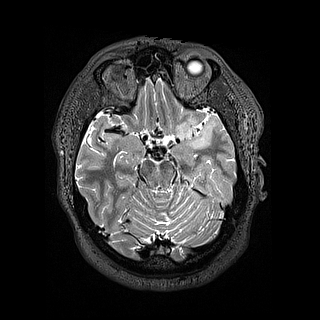
Brain MRI from a brain-tumour surgery series, one axial slice. 1.2 mm slice thickness. 320 × 320 image matrix, field of view 254 × 254 mm. From the clinical record (not read from this slice): histopathology: Astrocytoma; WHO grade: 2; IDH mutation: yes.
Annotated regions visible in this slice (outlined manually by an expert reader):
- tumour: box from (x=174, y=113) to (x=205, y=150) px